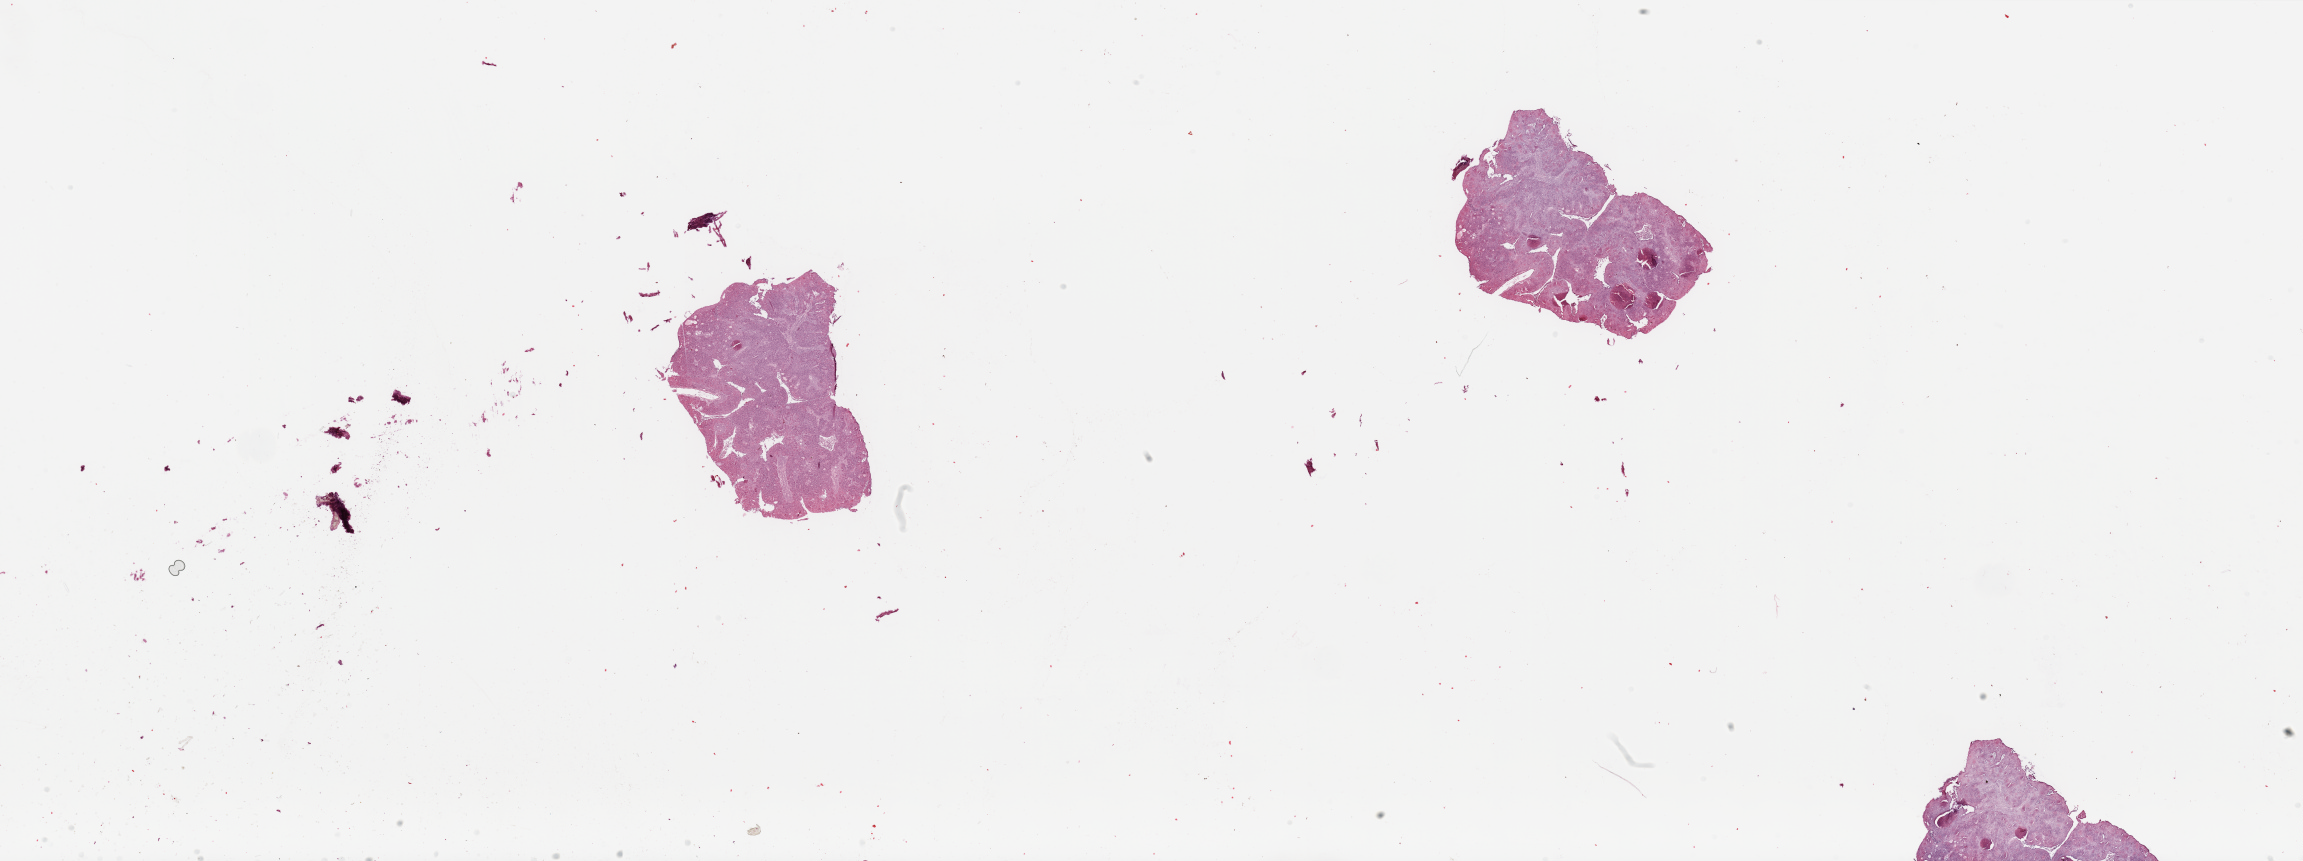
Whole-slide histology image, H&E-stained, whole scanned area (about 36.4 x 13.6 mm, from a 20x scan) shown as a low-resolution overview; tumour tissue sample, uterus. Female, 70 y/o.
Histologic diagnosis: Endometrioid adenocarcinoma, NOS.